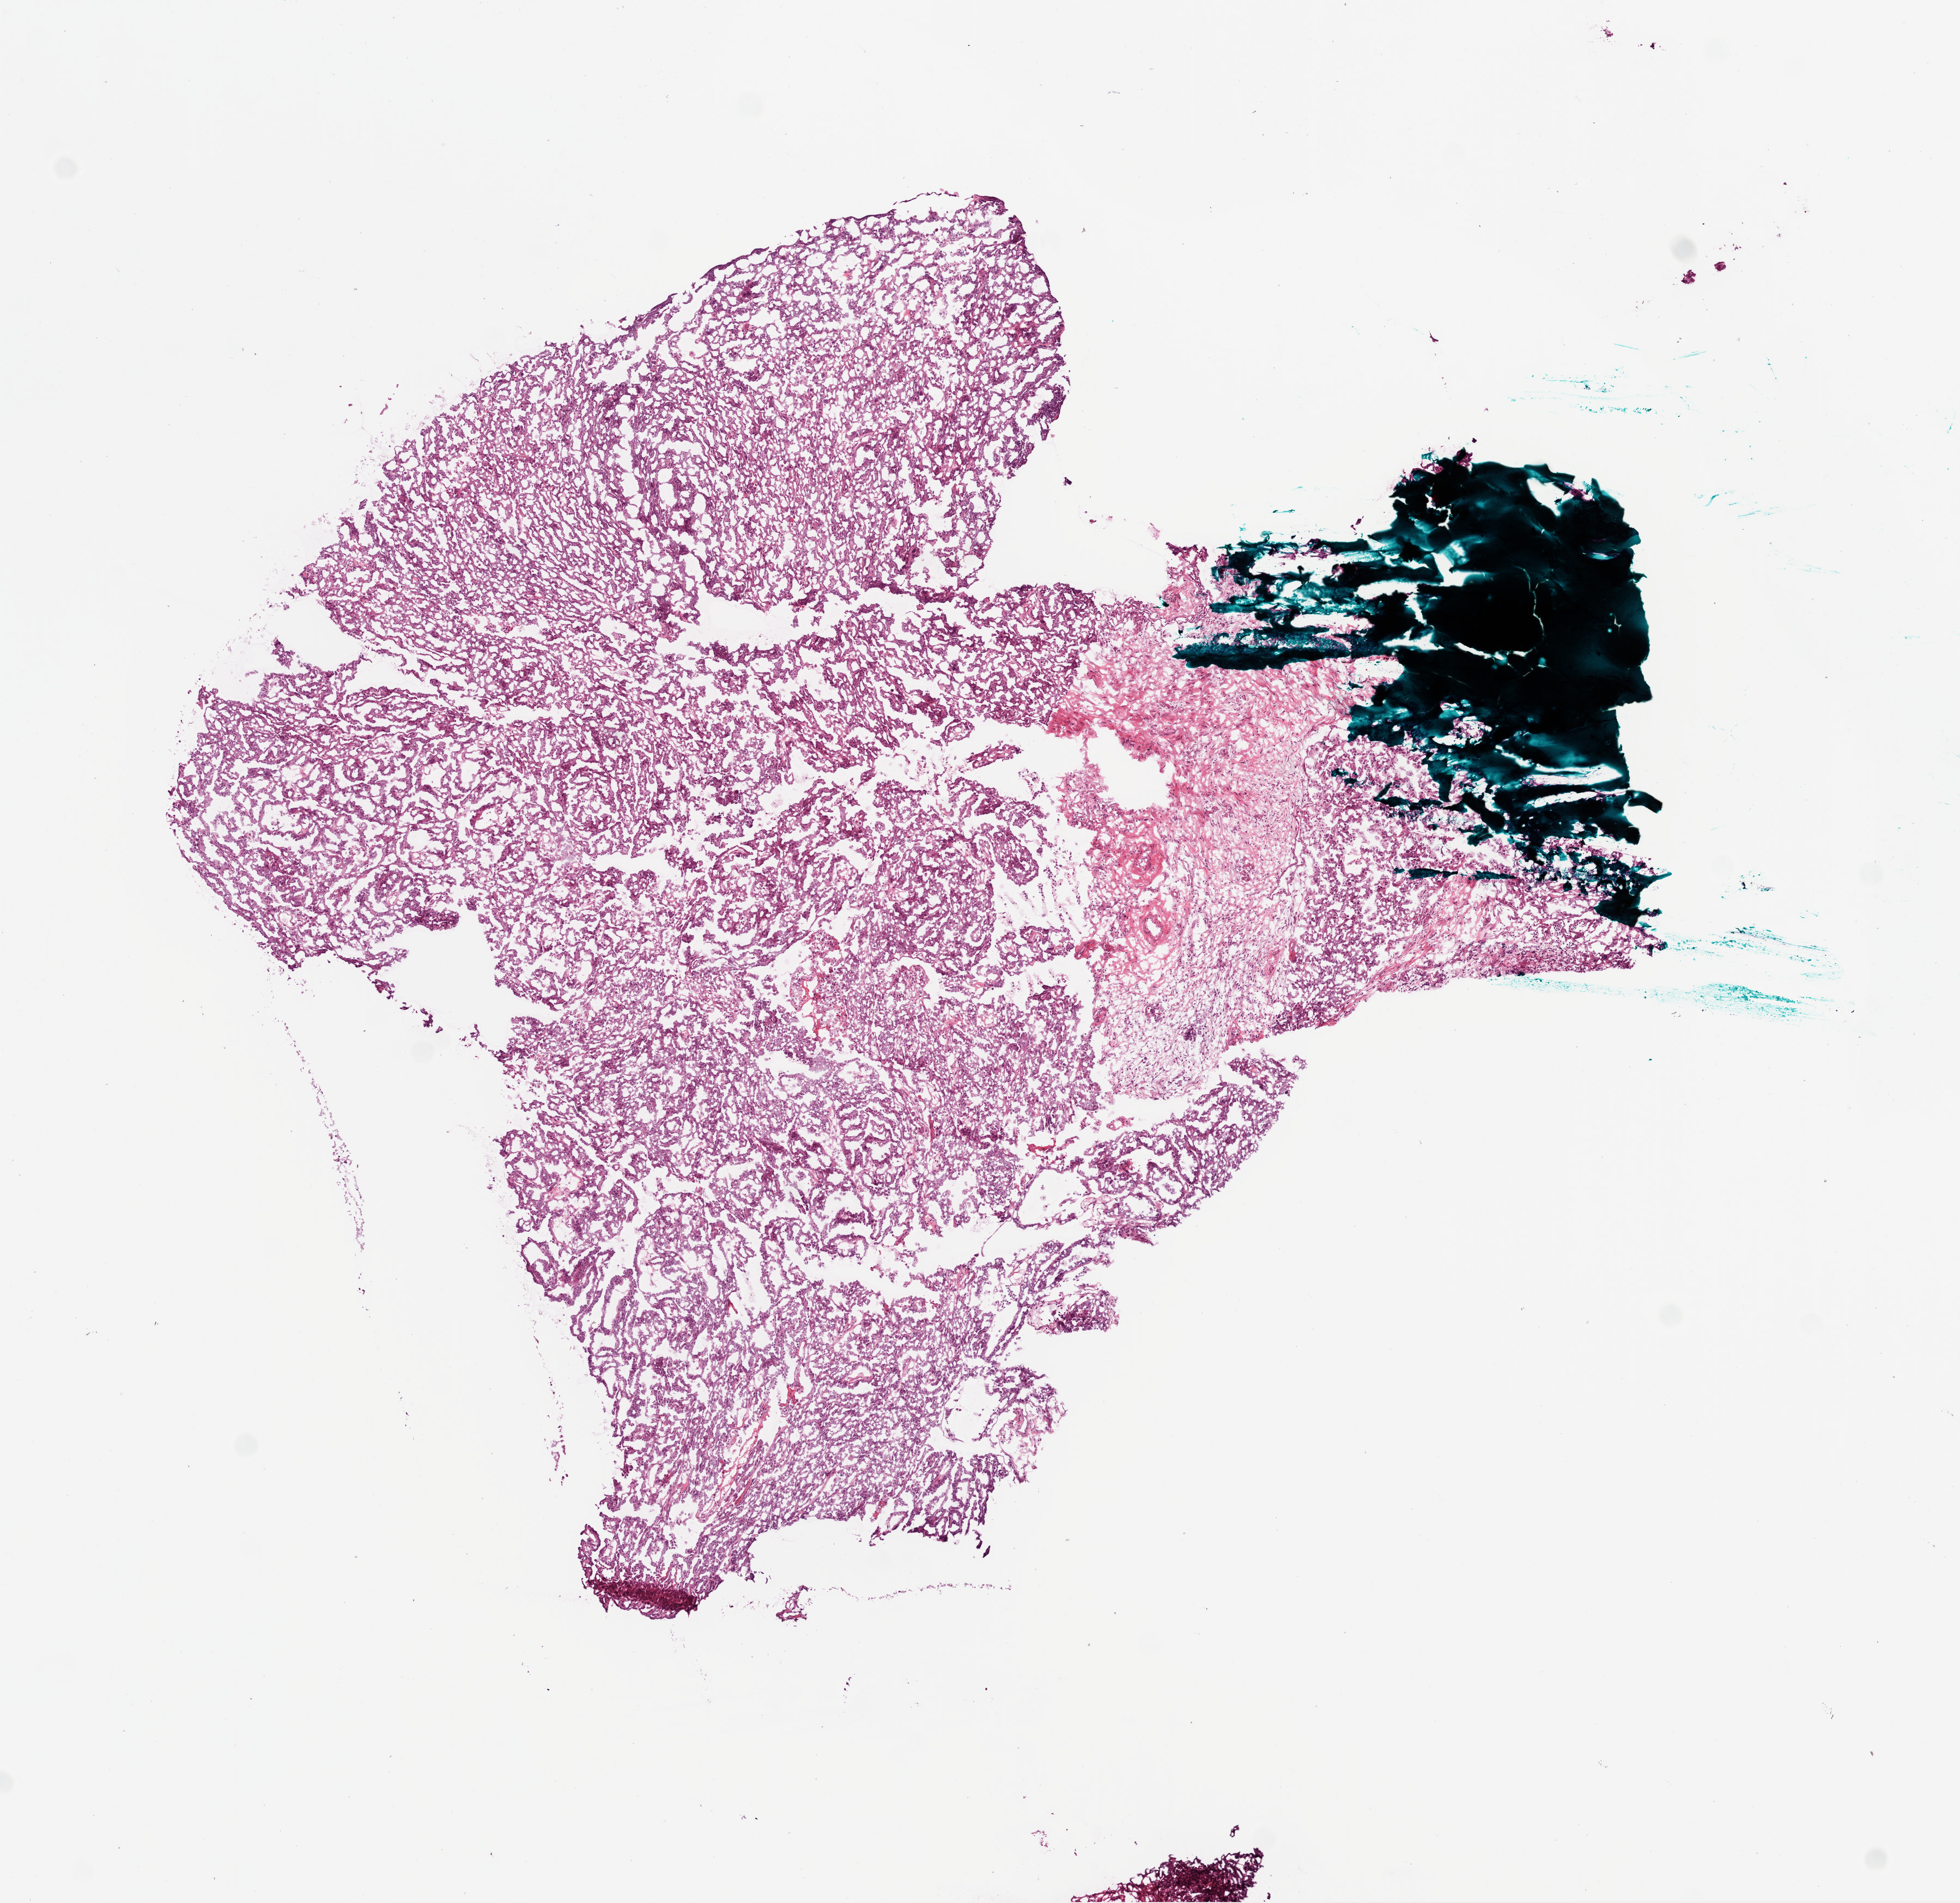
Whole-slide histology image, H&E — a low-resolution overview of the entire scanned area, about 7.3 x 7.0 mm (from a 20x scan); frozen section from the bottom of the tissue portion; ovary, primary tumour sample. Patient: female, age at initial diagnosis 64 years. Histologic grade: G3 (poorly differentiated). Slide review estimates, as recorded: tumour cells 85%, tumour nuclei 95%, normal cells 5%, stromal cells 5%, necrosis 5%.
Laterality: left. FIGO stage: IIIC. Diagnosis: Serous cystadenocarcinoma, NOS.